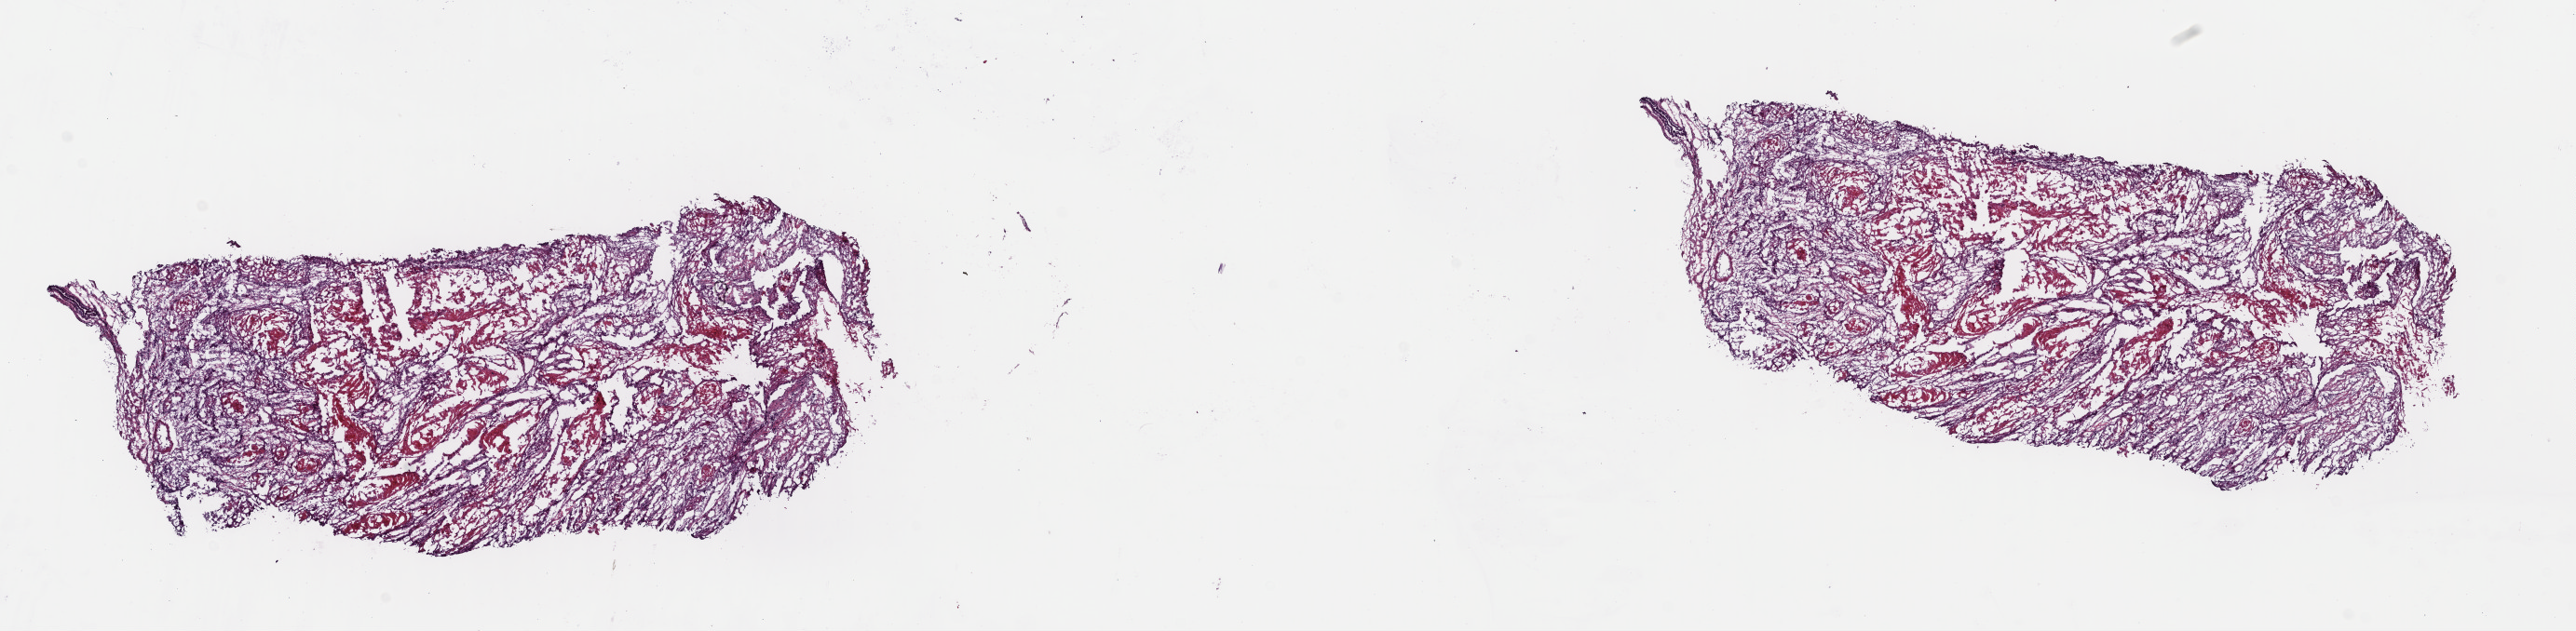
Hematoxylin and eosin (H&E) stained whole-slide image — shown as a low-resolution overview of the whole scanned area (about 21.7 x 5.3 mm). Frozen section. Sample: primary tumour, esophagus. Male, age 72 years at initial diagnosis.
Diagnosis: Squamous cell carcinoma, keratinizing, NOS.